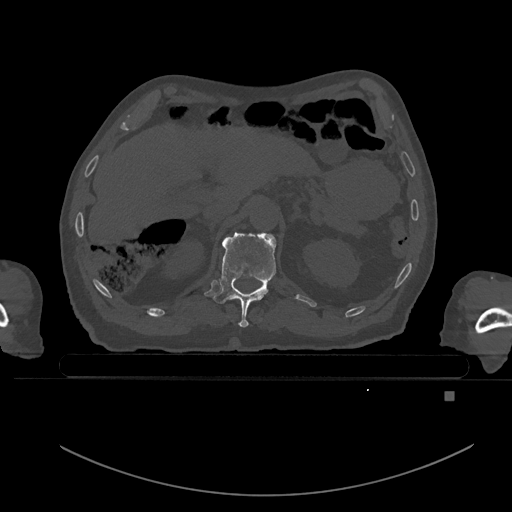
CT including the spine, one axial slice. Slice 23 of 969 in the series (ordered by position). Bone window (W 1800 / L 400 HU). 0.5 mm slice thickness. 512 × 512 image matrix, field of view 456 × 456 mm. Male patient, age 82 years. Case-level facts recorded for this patient, not image findings: primary cancer: prostate; vertebrae with lytic lesions (as recorded): T11, T9, T8, T2.
Outlined on this slice (semi-automatic segmentation, software-assisted and operator-edited):
- T11 vertebra: bounding box [x1, y1, x2, y2] px = [213, 233, 276, 328]